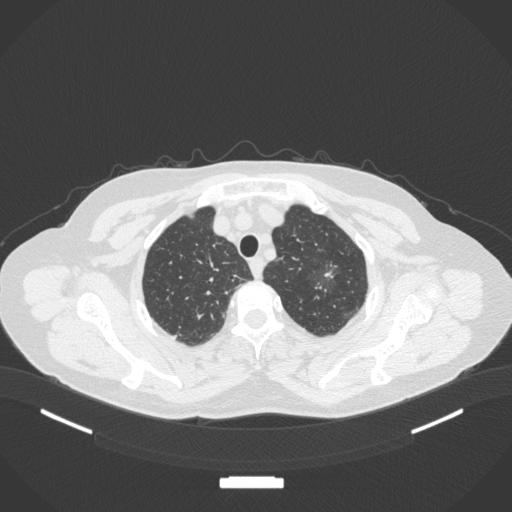
Chest CT, one axial slice; position 306 of 369 along the scan axis; 120 kVp; lung window (W 1500 / L -600 HU); 1 mm slice thickness; 512 × 512 image matrix. Female patient, age 64 years. From the clinical record (not read from this slice): clinical TNM (as recorded): T1c N0 M0; histopathological grade: G1.
Annotated regions visible in this slice (rectangle marked by the reading radiologist):
- lung tumour (recorded histology: adenocarcinoma): bounding box [x1, y1, x2, y2] px = [312, 252, 340, 286]